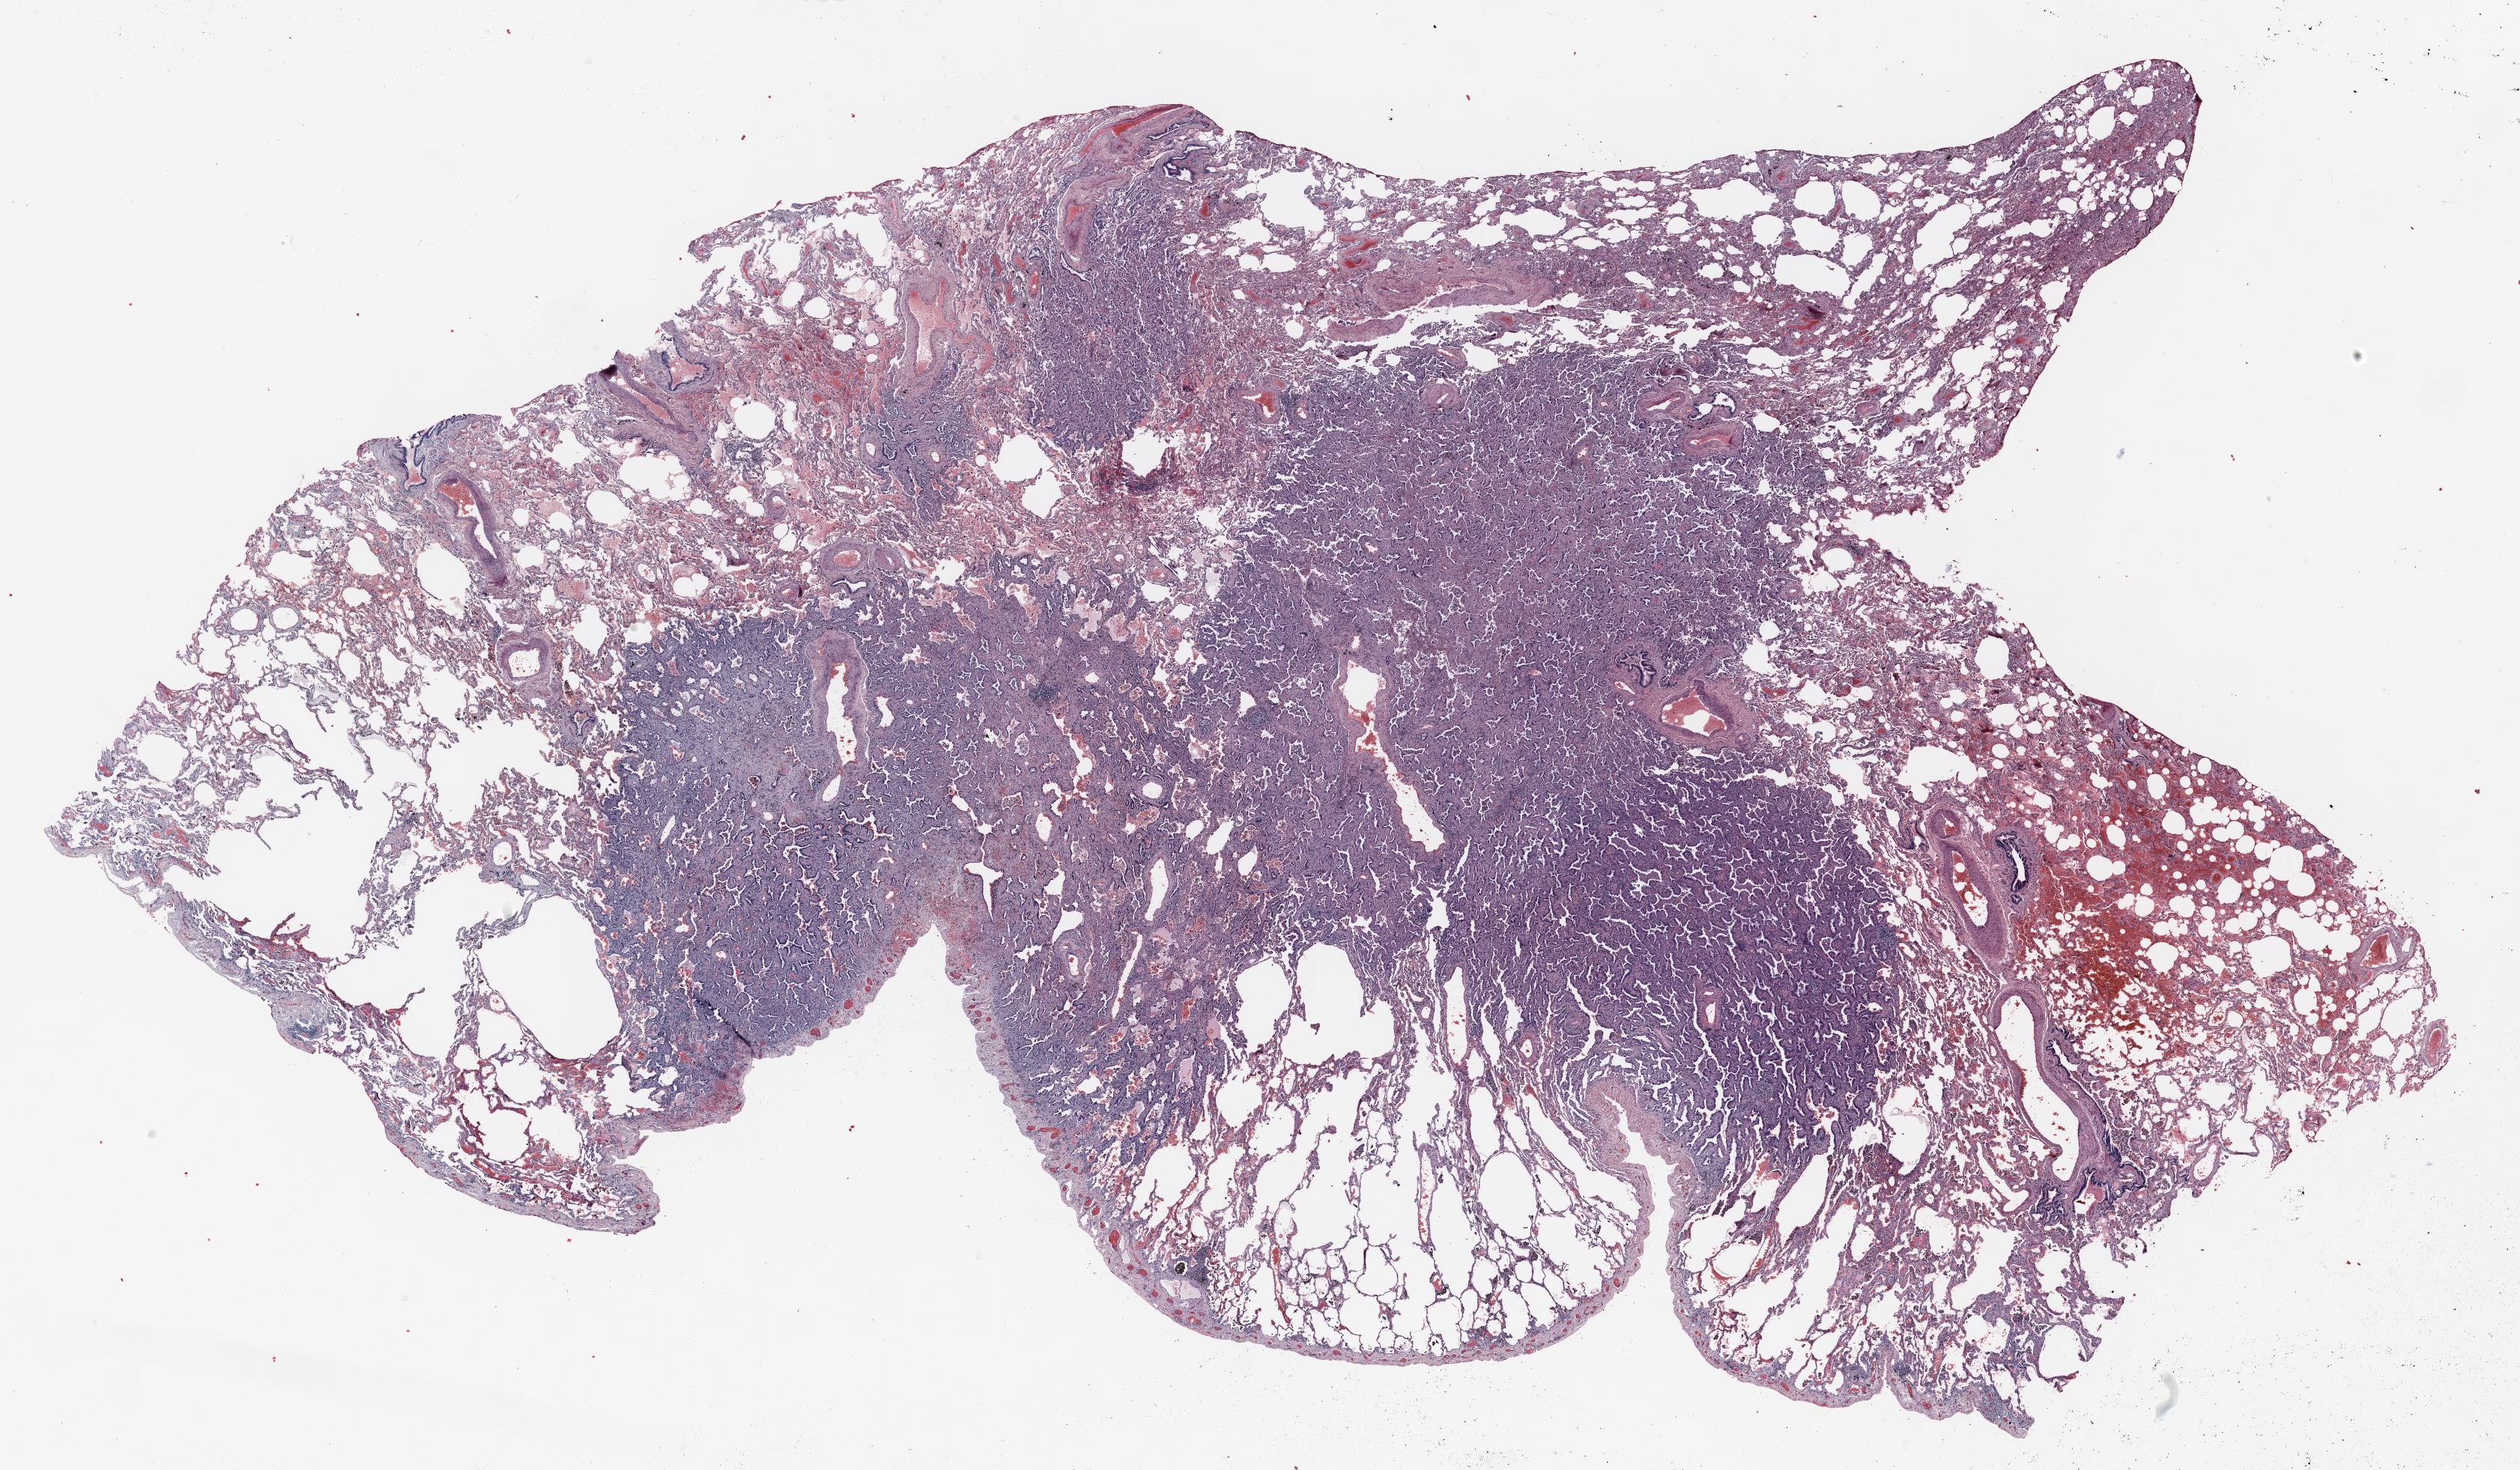
Whole-slide histology image, H&E, a low-resolution overview of the entire scanned area, about 27.0 x 15.8 mm (slide scanned at 20x), FFPE section, lung. Male, age 62 at enrolment.
- tumour size (pathology): 15 mm
- ICD-O-3 topography: upper lobe of lung (C34.1)
- stage (AJCC 6th edition): IA
- participant's lung-cancer diagnosis: Bronchiolo-alveolar adenocarcinoma, NOS
- primary tumour location (clinical record): left upper lobe